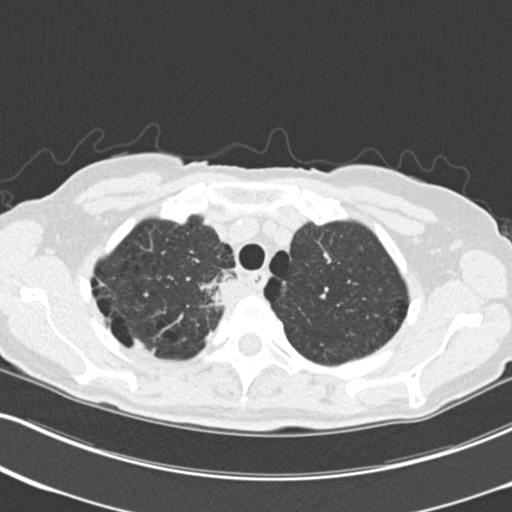
Low-dose screening chest CT, one axial slice. Position 184 of 226 along the scan axis. Reconstruction kernel B30f. Lung window (W 1500 / L -600 HU). 2 mm slice thickness. 512 × 512 image matrix, field of view 322 × 322 mm.
Outlined on this slice (expert manual segmentation):
- lesion 1 (tumor, mediastinum): box from (x=212, y=270) to (x=238, y=306) px